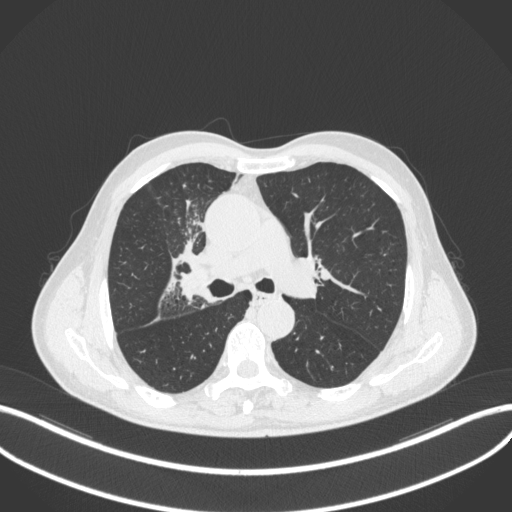
Chest CT, one axial slice. Slice 304 of 490 in the series (ordered by position). Reconstruction kernel B31f. 120 kVp. Lung window (W 1500 / L -600 HU). 1 mm slice thickness. 512 × 512 image matrix, field of view 400 × 400 mm. Patient: male, 69 years. Case-level facts recorded for this patient, not image findings: clinical TNM (as recorded): T2a N0 M0.
Annotated regions visible in this slice (bounding box drawn by a radiologist):
- lung tumour (recorded histology: adenocarcinoma): bounding box <177,264,204,305> (left, top, right, bottom; pixels)